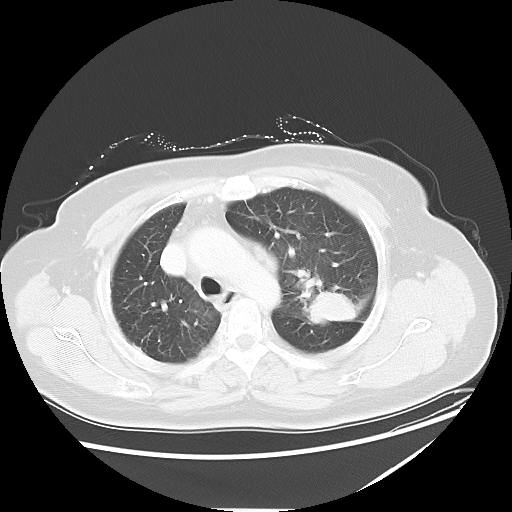
Chest CT, one axial slice; slice 40 of 54 in the series (ordered by position); reconstruction kernel LUNG; 120 kVp; lung window (W 1500 / L -600 HU); 5 mm slice thickness; 512 × 512 image matrix, field of view 384 × 384 mm. Female patient, age 61 years. From the clinical record (not read from this slice): clinical TNM (as recorded): T1c N3 M1.
Structures marked on this image (bounding box drawn by a radiologist):
- lung tumour (recorded histology: adenocarcinoma): bounding box (x1, y1, x2, y2) in pixels: (300, 288, 361, 328)